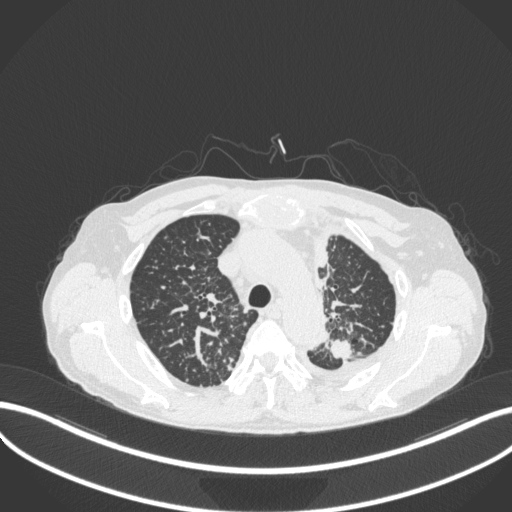
Chest CT, one axial slice. Position 268 of 319 along the scan axis. Reconstruction kernel B31f. 120 kVp. Lung window (W 1500 / L -600 HU). 512 × 512 image matrix. Male patient, age 58 years. From the clinical record (not read from this slice): clinical TNM (as recorded): T1c N3 M1.
Structures marked on this image (bounding box drawn by a radiologist):
- lung tumour (recorded histology: adenocarcinoma): box from (x=326, y=336) to (x=355, y=364) px